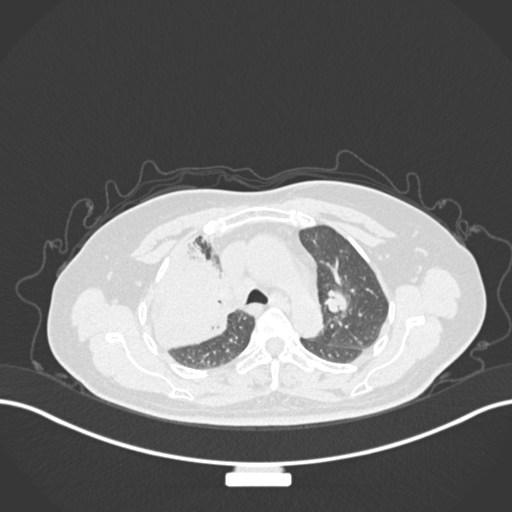
Chest CT, one axial slice; slice 109 of 177 in the series (ordered by position); reconstruction kernel B30f; lung window (W 1500 / L -600 HU); 1 mm slice thickness; 512 × 512 image matrix, field of view 400 × 400 mm. Female patient, age 60 years. Case-level facts recorded for this patient, not image findings: clinical TNM (as recorded): T3 N1 M1.
Structures marked on this image (rectangle marked by the reading radiologist):
- lung tumour (recorded histology: adenocarcinoma): bounding box <139,235,240,357> (left, top, right, bottom; pixels)